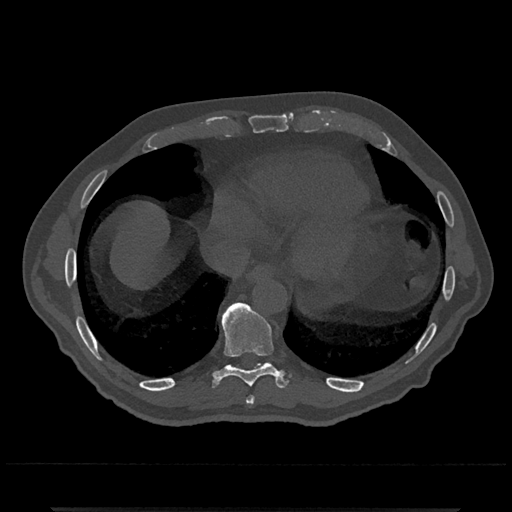
CT including the spine, one axial slice. Slice 608 of 797 in the series (ordered by position). Reconstruction kernel Br40s/3. 120 kVp. Bone window (W 1800 / L 400 HU). 512 × 512 image matrix, field of view 393 × 393 mm. Patient: male, 67 years. Case-level facts recorded for this patient, not image findings: primary cancer: prostate.
Outlined on this slice (semi-automatic segmentation, software-assisted and operator-edited):
- T8 vertebra: bounding box <247,396,255,404> (left, top, right, bottom; pixels)
- T9 vertebra: <214,302,286,388>